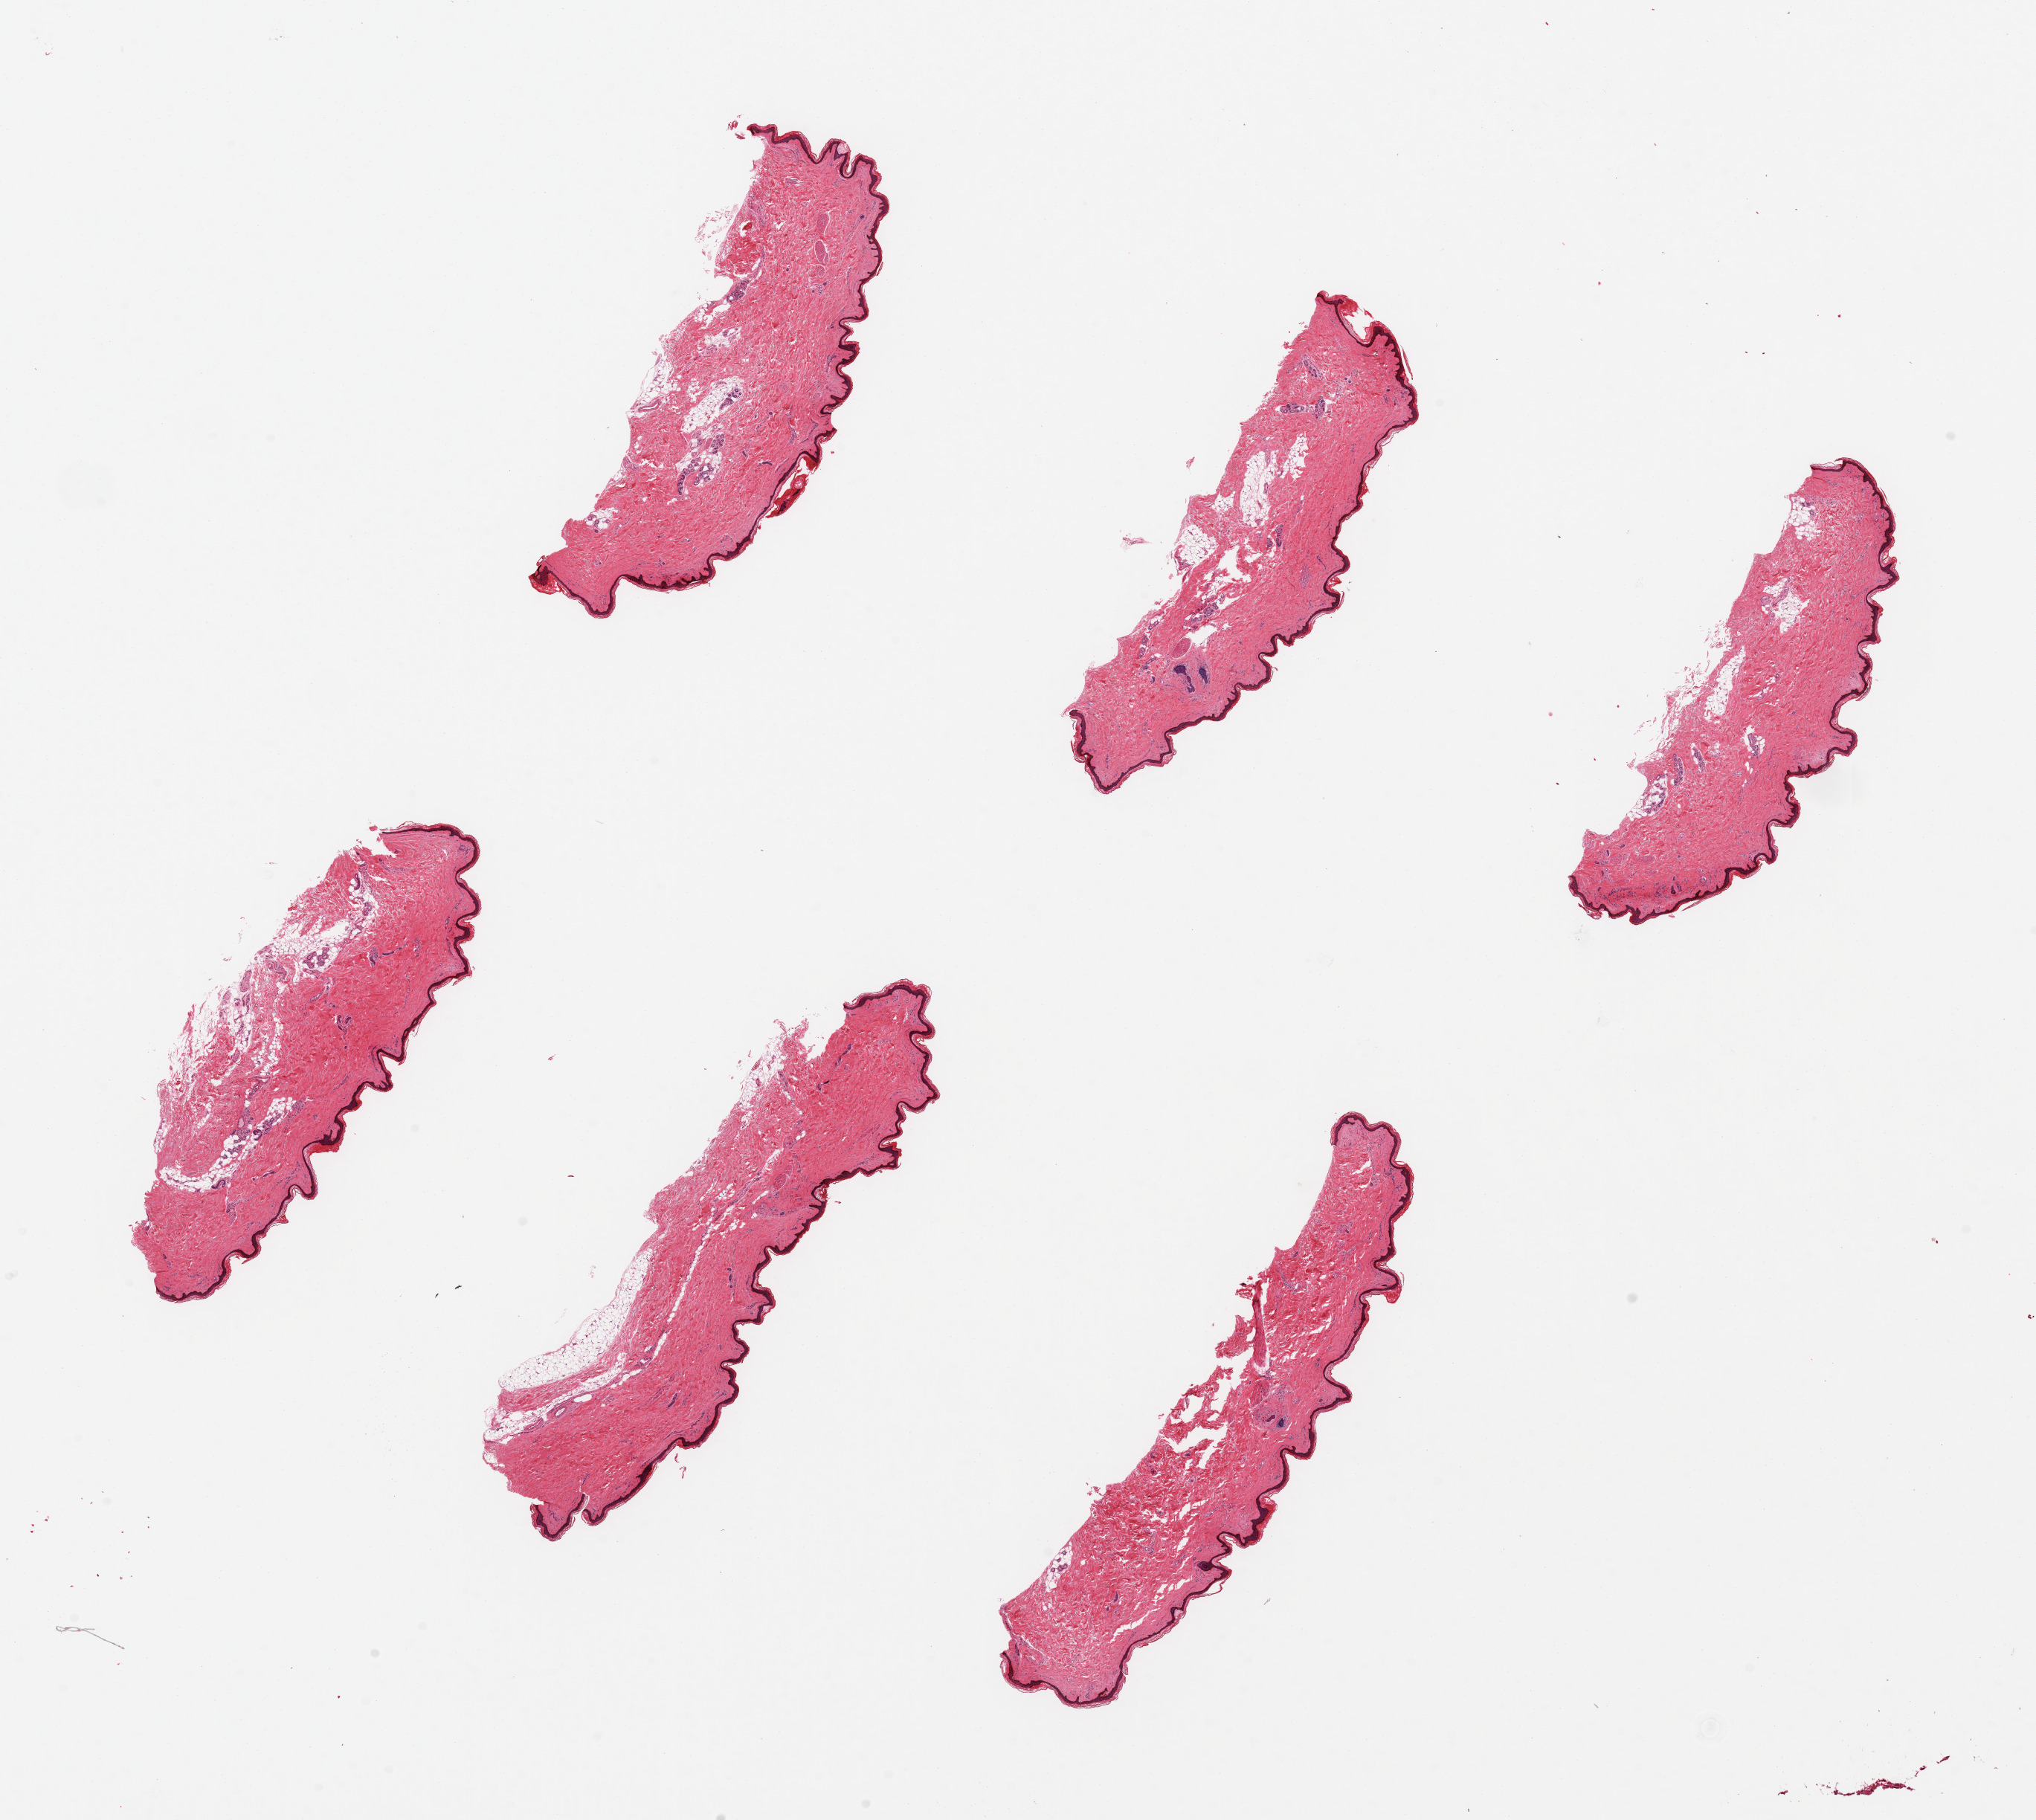
Digitized hematoxylin and eosin (H&E)-stained section — whole scanned area (about 21.7 x 19.4 mm) shown as a low-resolution overview, PAXgene-fixed paraffin-embedded (PFPE) section, section of skin of lower leg (target tissue), tissue donor sample. Male donor.
• reviewer comment on this tissue sample: 6 pieces ~6x1.5mm Squamous epithelium is ~2-3% thickness